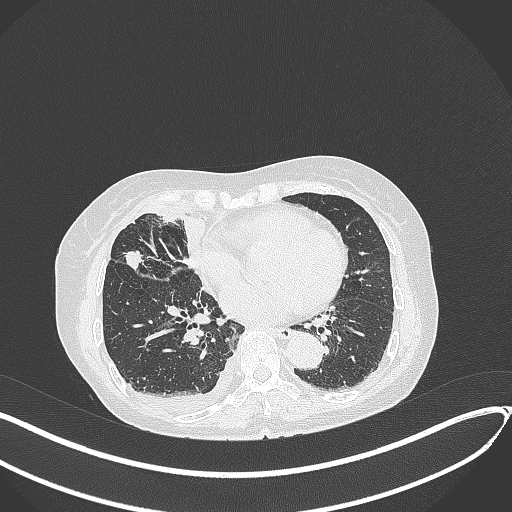
Chest CT, one axial slice; slice 160 of 418 in the series (ordered by position); reconstruction kernel B70f; 120 kVp; lung window (W 1500 / L -600 HU); 1 mm slice thickness; 512 × 512 image matrix. Patient: female, 75 years. From the clinical record (not read from this slice): clinical TNM (as recorded): T2a N3 M0.
Structures marked on this image (bounding box drawn by a radiologist):
- lung tumour (recorded histology: adenocarcinoma): bounding box <122,246,148,274> (left, top, right, bottom; pixels)